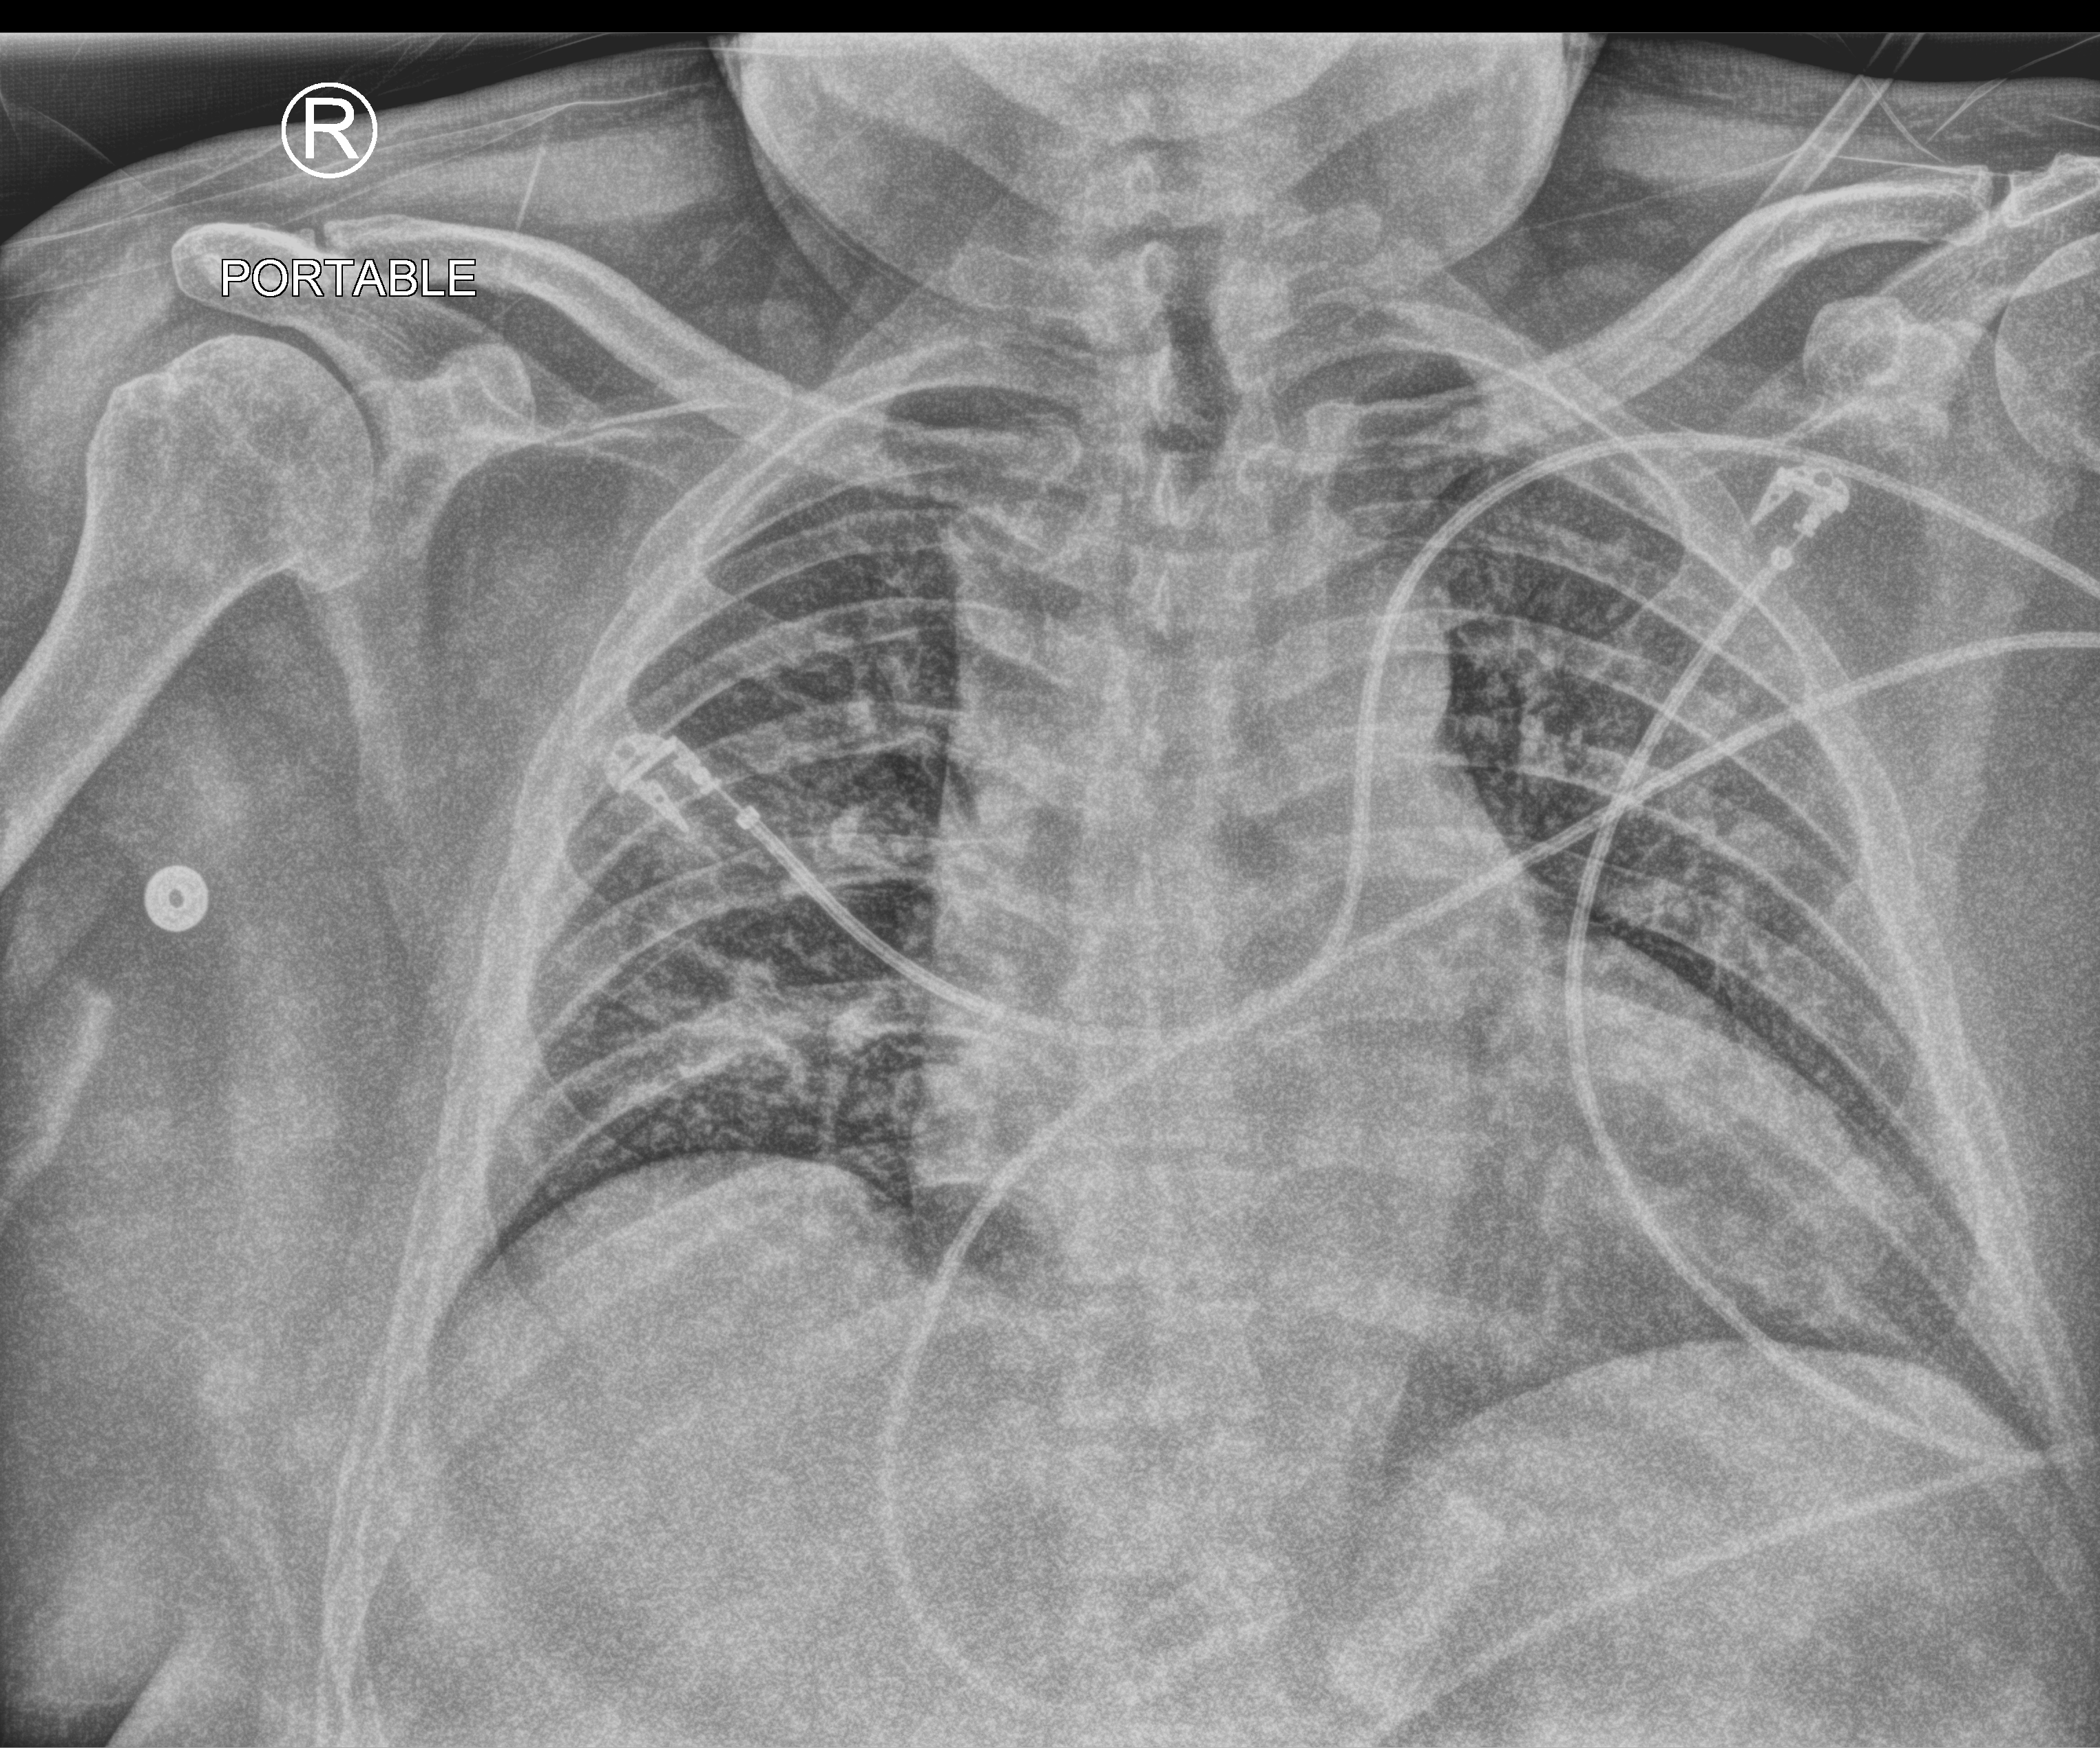
Chest X-ray (portable), anteroposterior (AP) projection. Patient hospitalised with COVID-19; male, aged 60–74 years.
From the hospital-stay record, not from the radiograph (when in the stay this image was taken is not recorded):
- admitted to intensive care during this hospital stay: yes
- mechanically ventilated during this hospital stay: yes
- smoking status (admission record): former